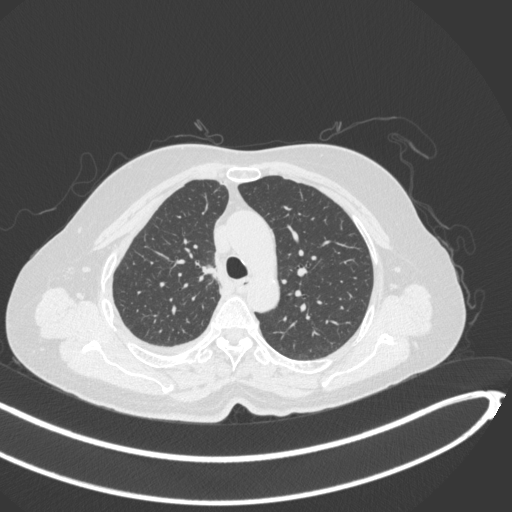
Chest CT, one axial slice; slice 218 of 297 in the series (ordered by position); reconstruction kernel B31f; 120 kVp; lung window (W 1500 / L -600 HU); 1 mm slice thickness; 512 × 512 image matrix, field of view 400 × 400 mm. Patient: female, 64 years. From the clinical record (not read from this slice): clinical TNM (as recorded): T1b N0 M1.
Structures marked on this image (bounding box drawn by a radiologist):
- lung tumour (recorded histology: adenocarcinoma): box from (x=196, y=257) to (x=219, y=286) px